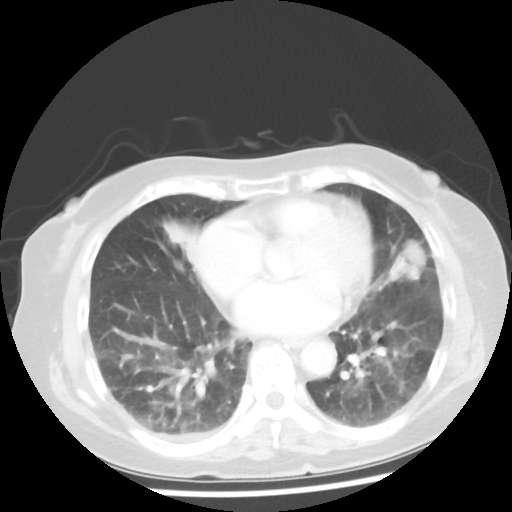
Chest CT, one axial slice. Slice 19 of 50 in the series (ordered by position). 100 kVp. Lung window (W 1500 / L -600 HU). 5 mm slice thickness. 512 × 512 image matrix, field of view 332 × 332 mm. Female patient, age 77 years. Case-level facts recorded for this patient, not image findings: clinical TNM (as recorded): T2 N3 M1a.
Annotated regions visible in this slice (bounding box drawn by a radiologist):
- lung tumour (recorded histology: adenocarcinoma): bounding box [x1, y1, x2, y2] px = [383, 233, 435, 293]